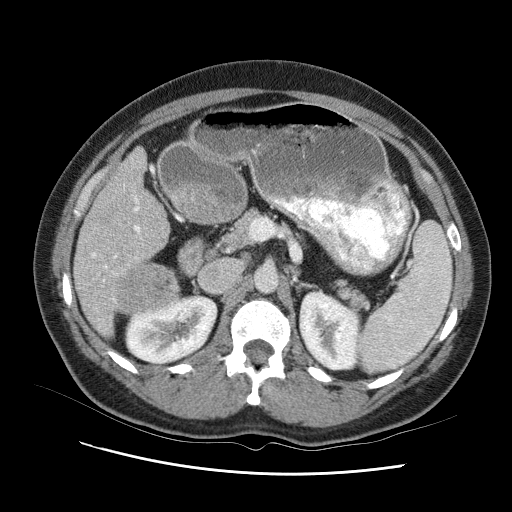
Contrast-enhanced abdominal CT (liver protocol), one axial slice; one of 2 acquisitions stored at this slice position; soft-tissue window (W 400 / L 40 HU); 2.5 mm slice thickness; 512 × 512 image matrix, field of view 360 × 360 mm. Case-level facts recorded for this patient, not image findings: diagnosis: hepatocellular carcinoma (patient treated with transarterial chemoembolisation; whether this scan precedes or follows treatment is not stated here); TNM stage (as recorded): Stage-I; Child-Pugh class: B; tumour differentiation: moderately differentiated.
Annotated regions visible in this slice (semi-automatically segmented with operator editing):
- liver parenchyma outside the tumour (the mass and vessels are separate outlines, so this box may not span the whole liver): bounding box (x1, y1, x2, y2) in pixels: (72, 138, 182, 352)
- mass: (116, 249, 186, 316)
- liver vessels: (89, 161, 166, 321)